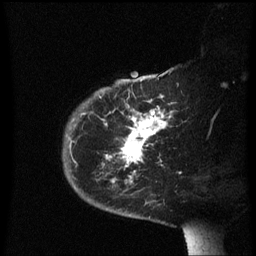
Breast MRI (dynamic contrast-enhanced), one sagittal slice; position 45 of 60 along the scan axis; dynamic contrast-enhanced series, image 2 of 3 at this slice position (ordered by acquisition); 1.5 T; TE 4.2 ms, TR 8.4 ms; 2.3 mm slice thickness; 256 × 256 image matrix, field of view 200 × 200 mm. Female patient, age 38 years. From the clinical record (not read from this slice): setting: breast cancer imaged before/during neoadjuvant chemotherapy; receptor status: HER2-positive.
Structures marked on this image (semi-automatic segmentation, software-assisted and operator-edited):
- analysis volume of interest (the breast-tissue region the enhancement analysis was run in; not a lesion): bounding box [x1, y1, x2, y2] px = [62, 78, 186, 213]
- tumour enhancement mask (voxels above the 70 % enhancement threshold inside the analysis volume of interest): [105, 108, 172, 183]